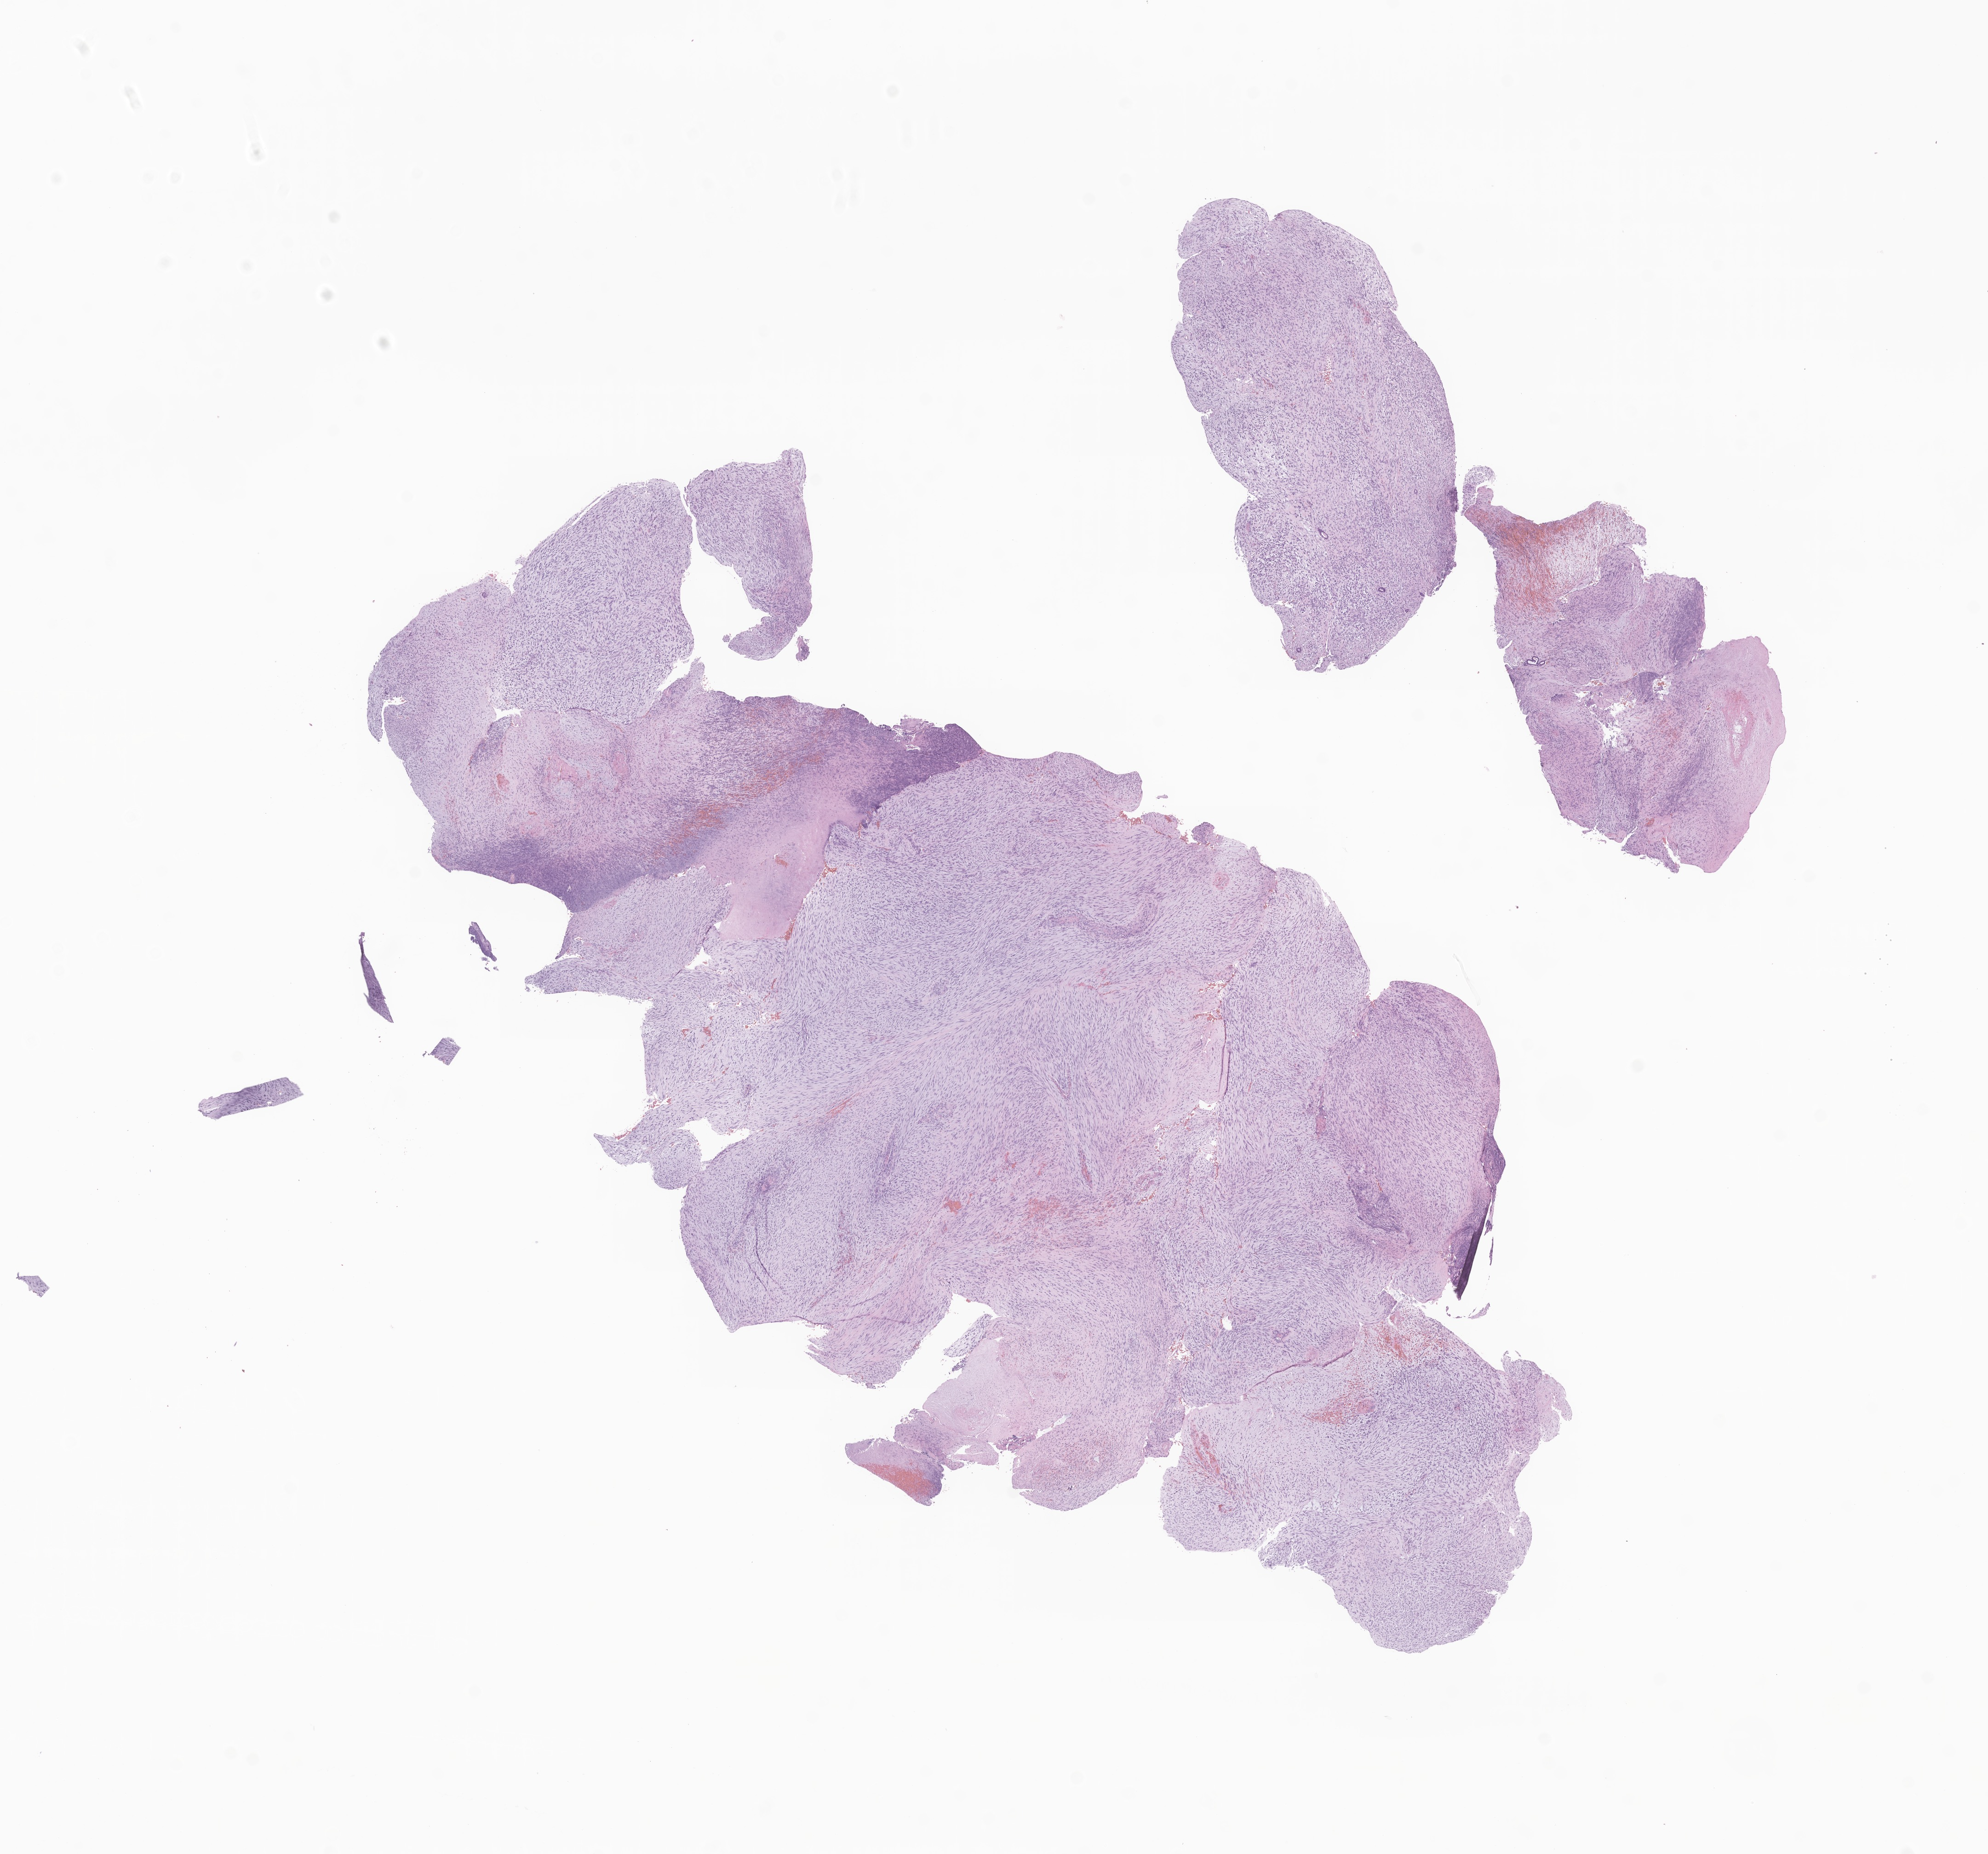
H&E whole-slide image of tumor tissue from the soft tissues of head and neck — low-resolution overview of the scanned area, about 18.2 x 17.0 mm. Formalin-fixed paraffin-embedded section. Patient: male, age 69 months (5 years 9 months).
• tissue or organ of origin (case record): connective, subcutaneous and other soft tissues of head, face, and neck
• recorded diagnosis: Sarcoma, NOS